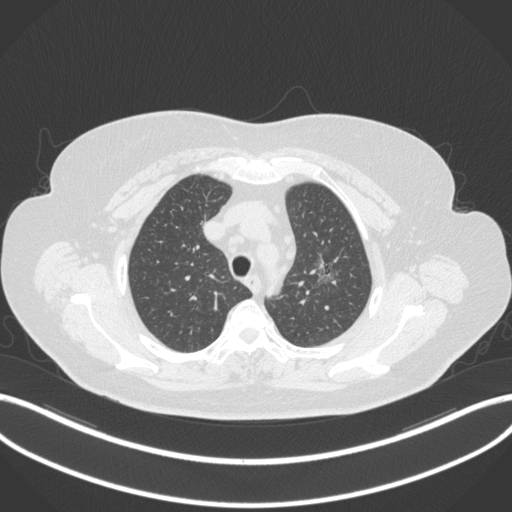
Chest CT, one axial slice; slice 266 of 310 in the series (ordered by position); 120 kVp; lung window (W 1500 / L -600 HU); 1 mm slice thickness; 512 × 512 image matrix, field of view 400 × 400 mm. Female patient, age 70 years. Case-level facts recorded for this patient, not image findings: clinical TNM (as recorded): T1c N0 M0.
Outlined on this slice (bounding box drawn by a radiologist):
- lung tumour (recorded histology: adenocarcinoma): bounding box (x1, y1, x2, y2) in pixels: (307, 252, 344, 293)